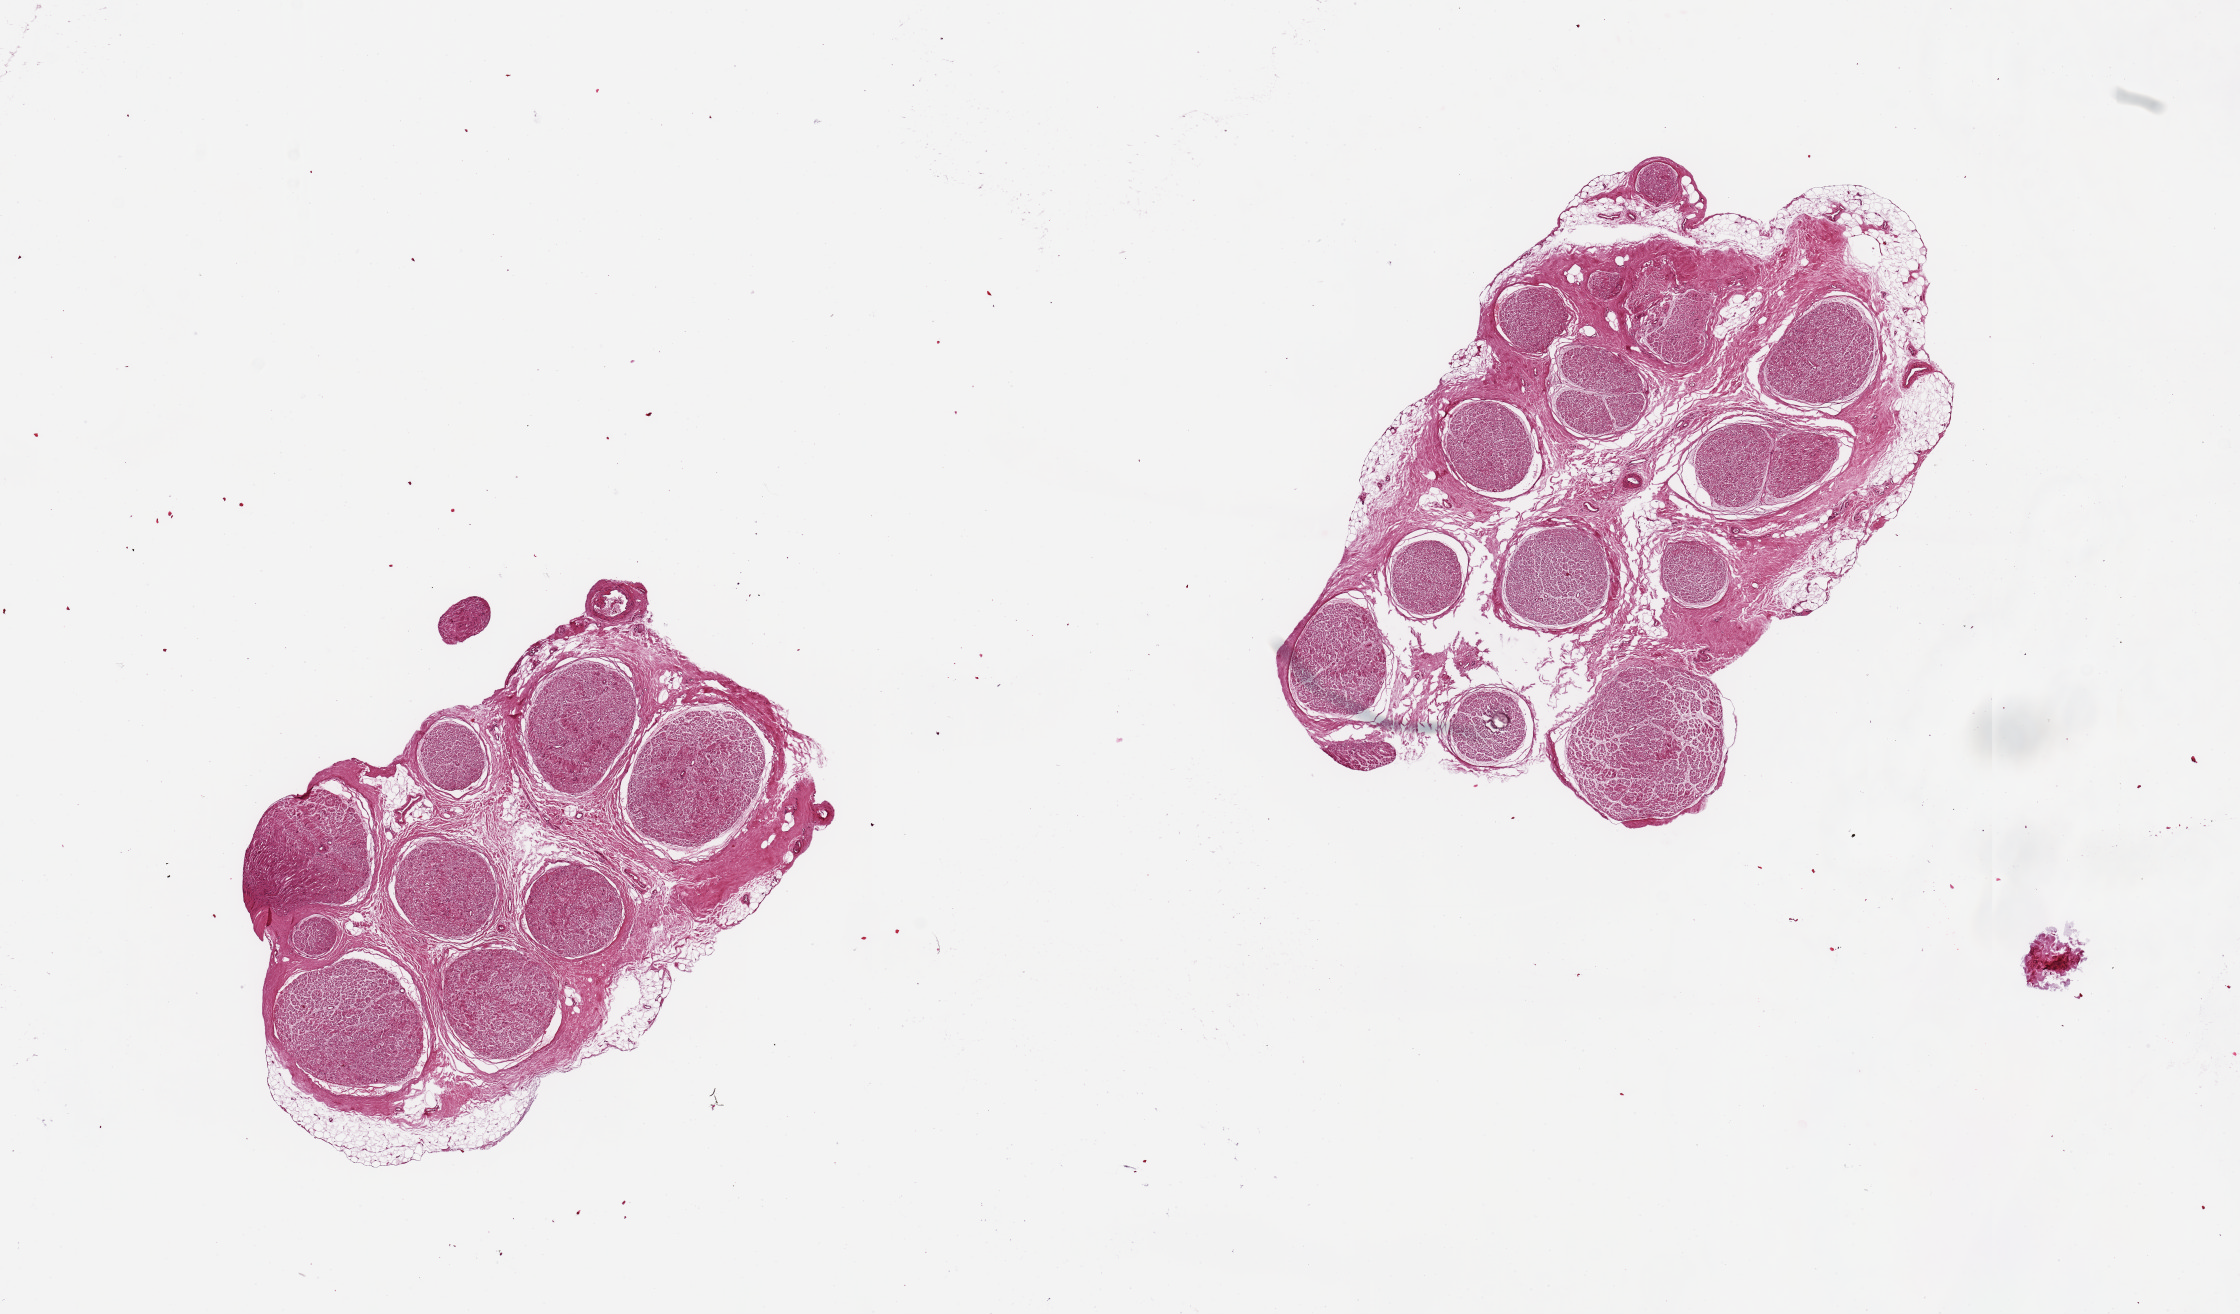
Whole-slide image, H&E stain — low-resolution overview of the scanned area, about 17.7 x 10.4 mm (slide scanned at 20x), PAXgene-fixed paraffin-embedded (PFPE) section, section of tibial nerve (target tissue), tissue donor sample.
- reviewer comment on this tissue sample: 2 pieces, 5x3 & 5x3.5mm; <10% adipose